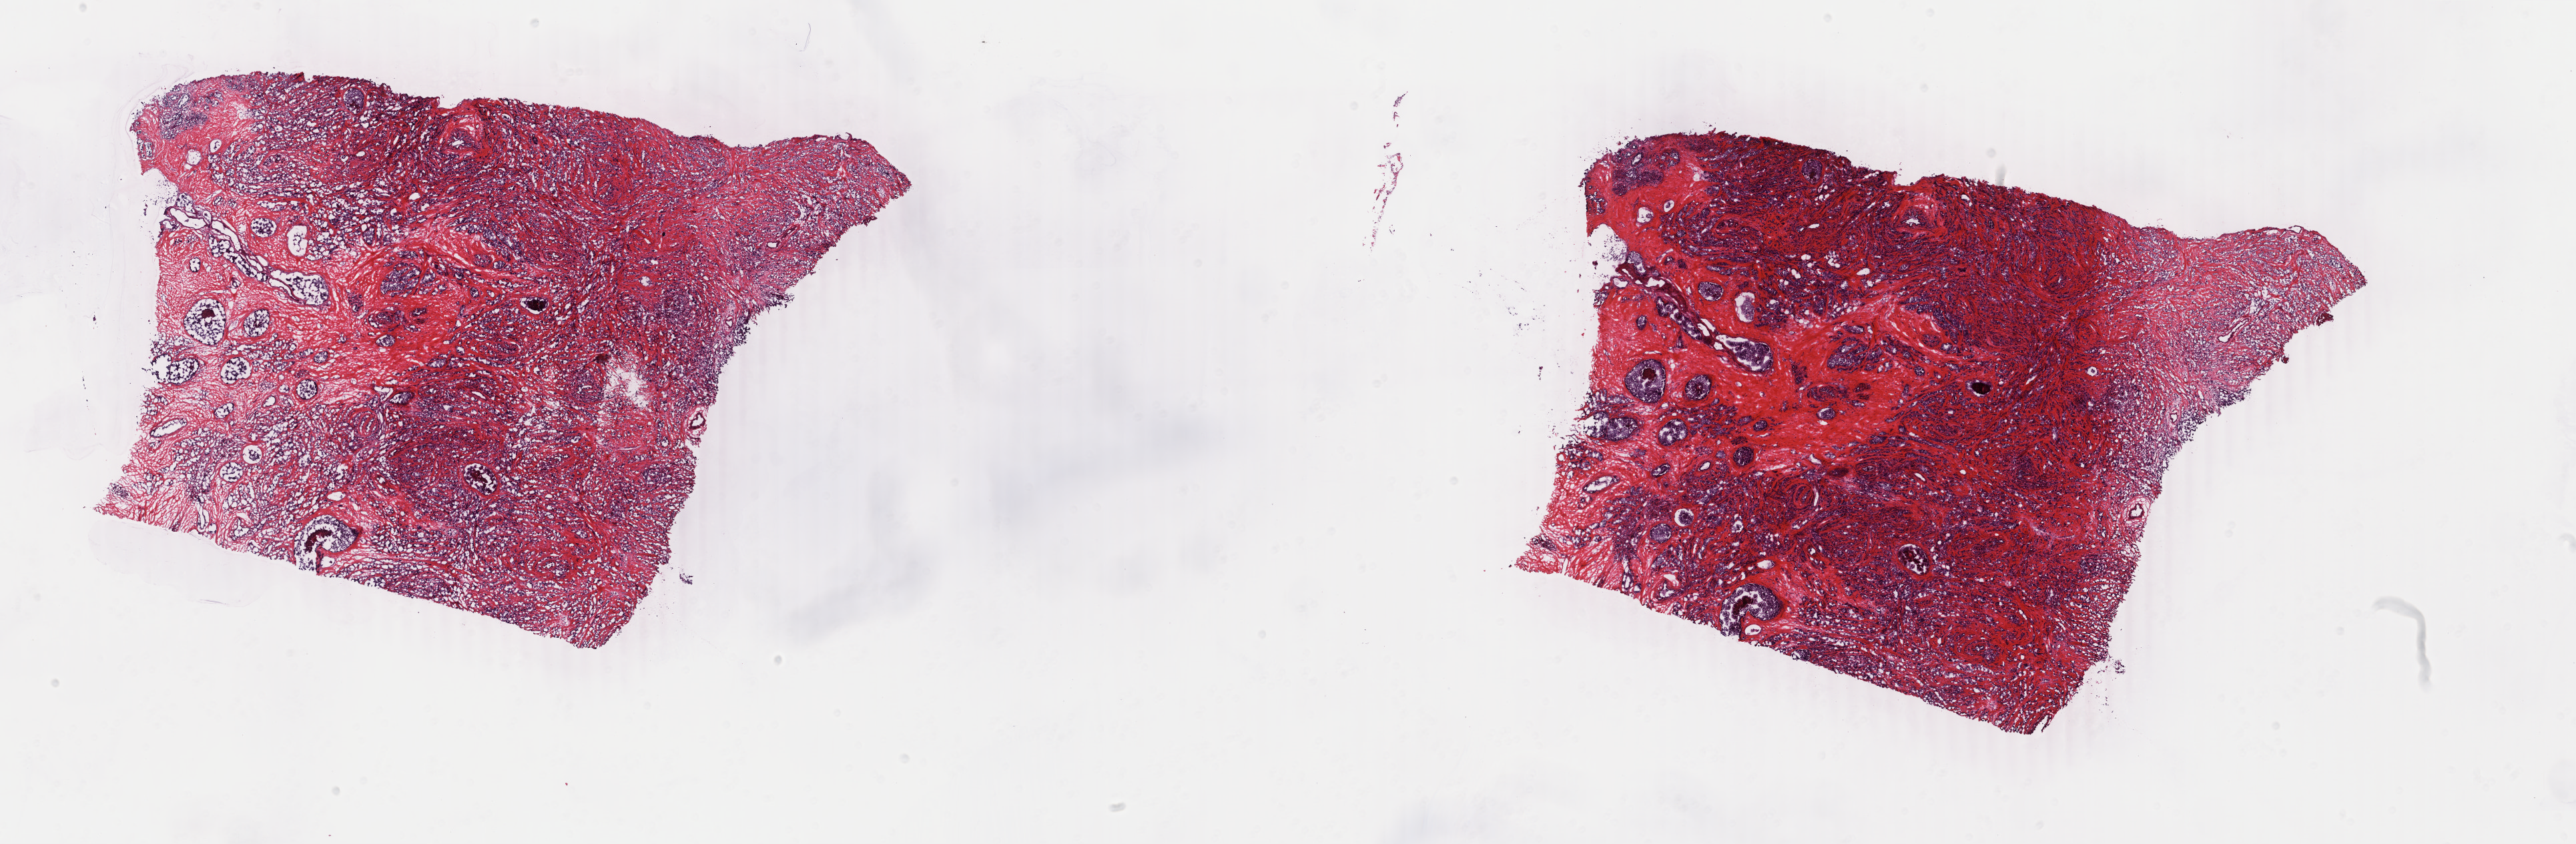
Digitized H&E tissue section (whole slide) — low-resolution overview of the scanned area, about 30.7 x 10.1 mm (from a 40x scan); frozen section; sample: primary tumour, breast. Female patient; age at initial diagnosis 50 years.
Diagnosis: Infiltrating duct carcinoma, NOS.